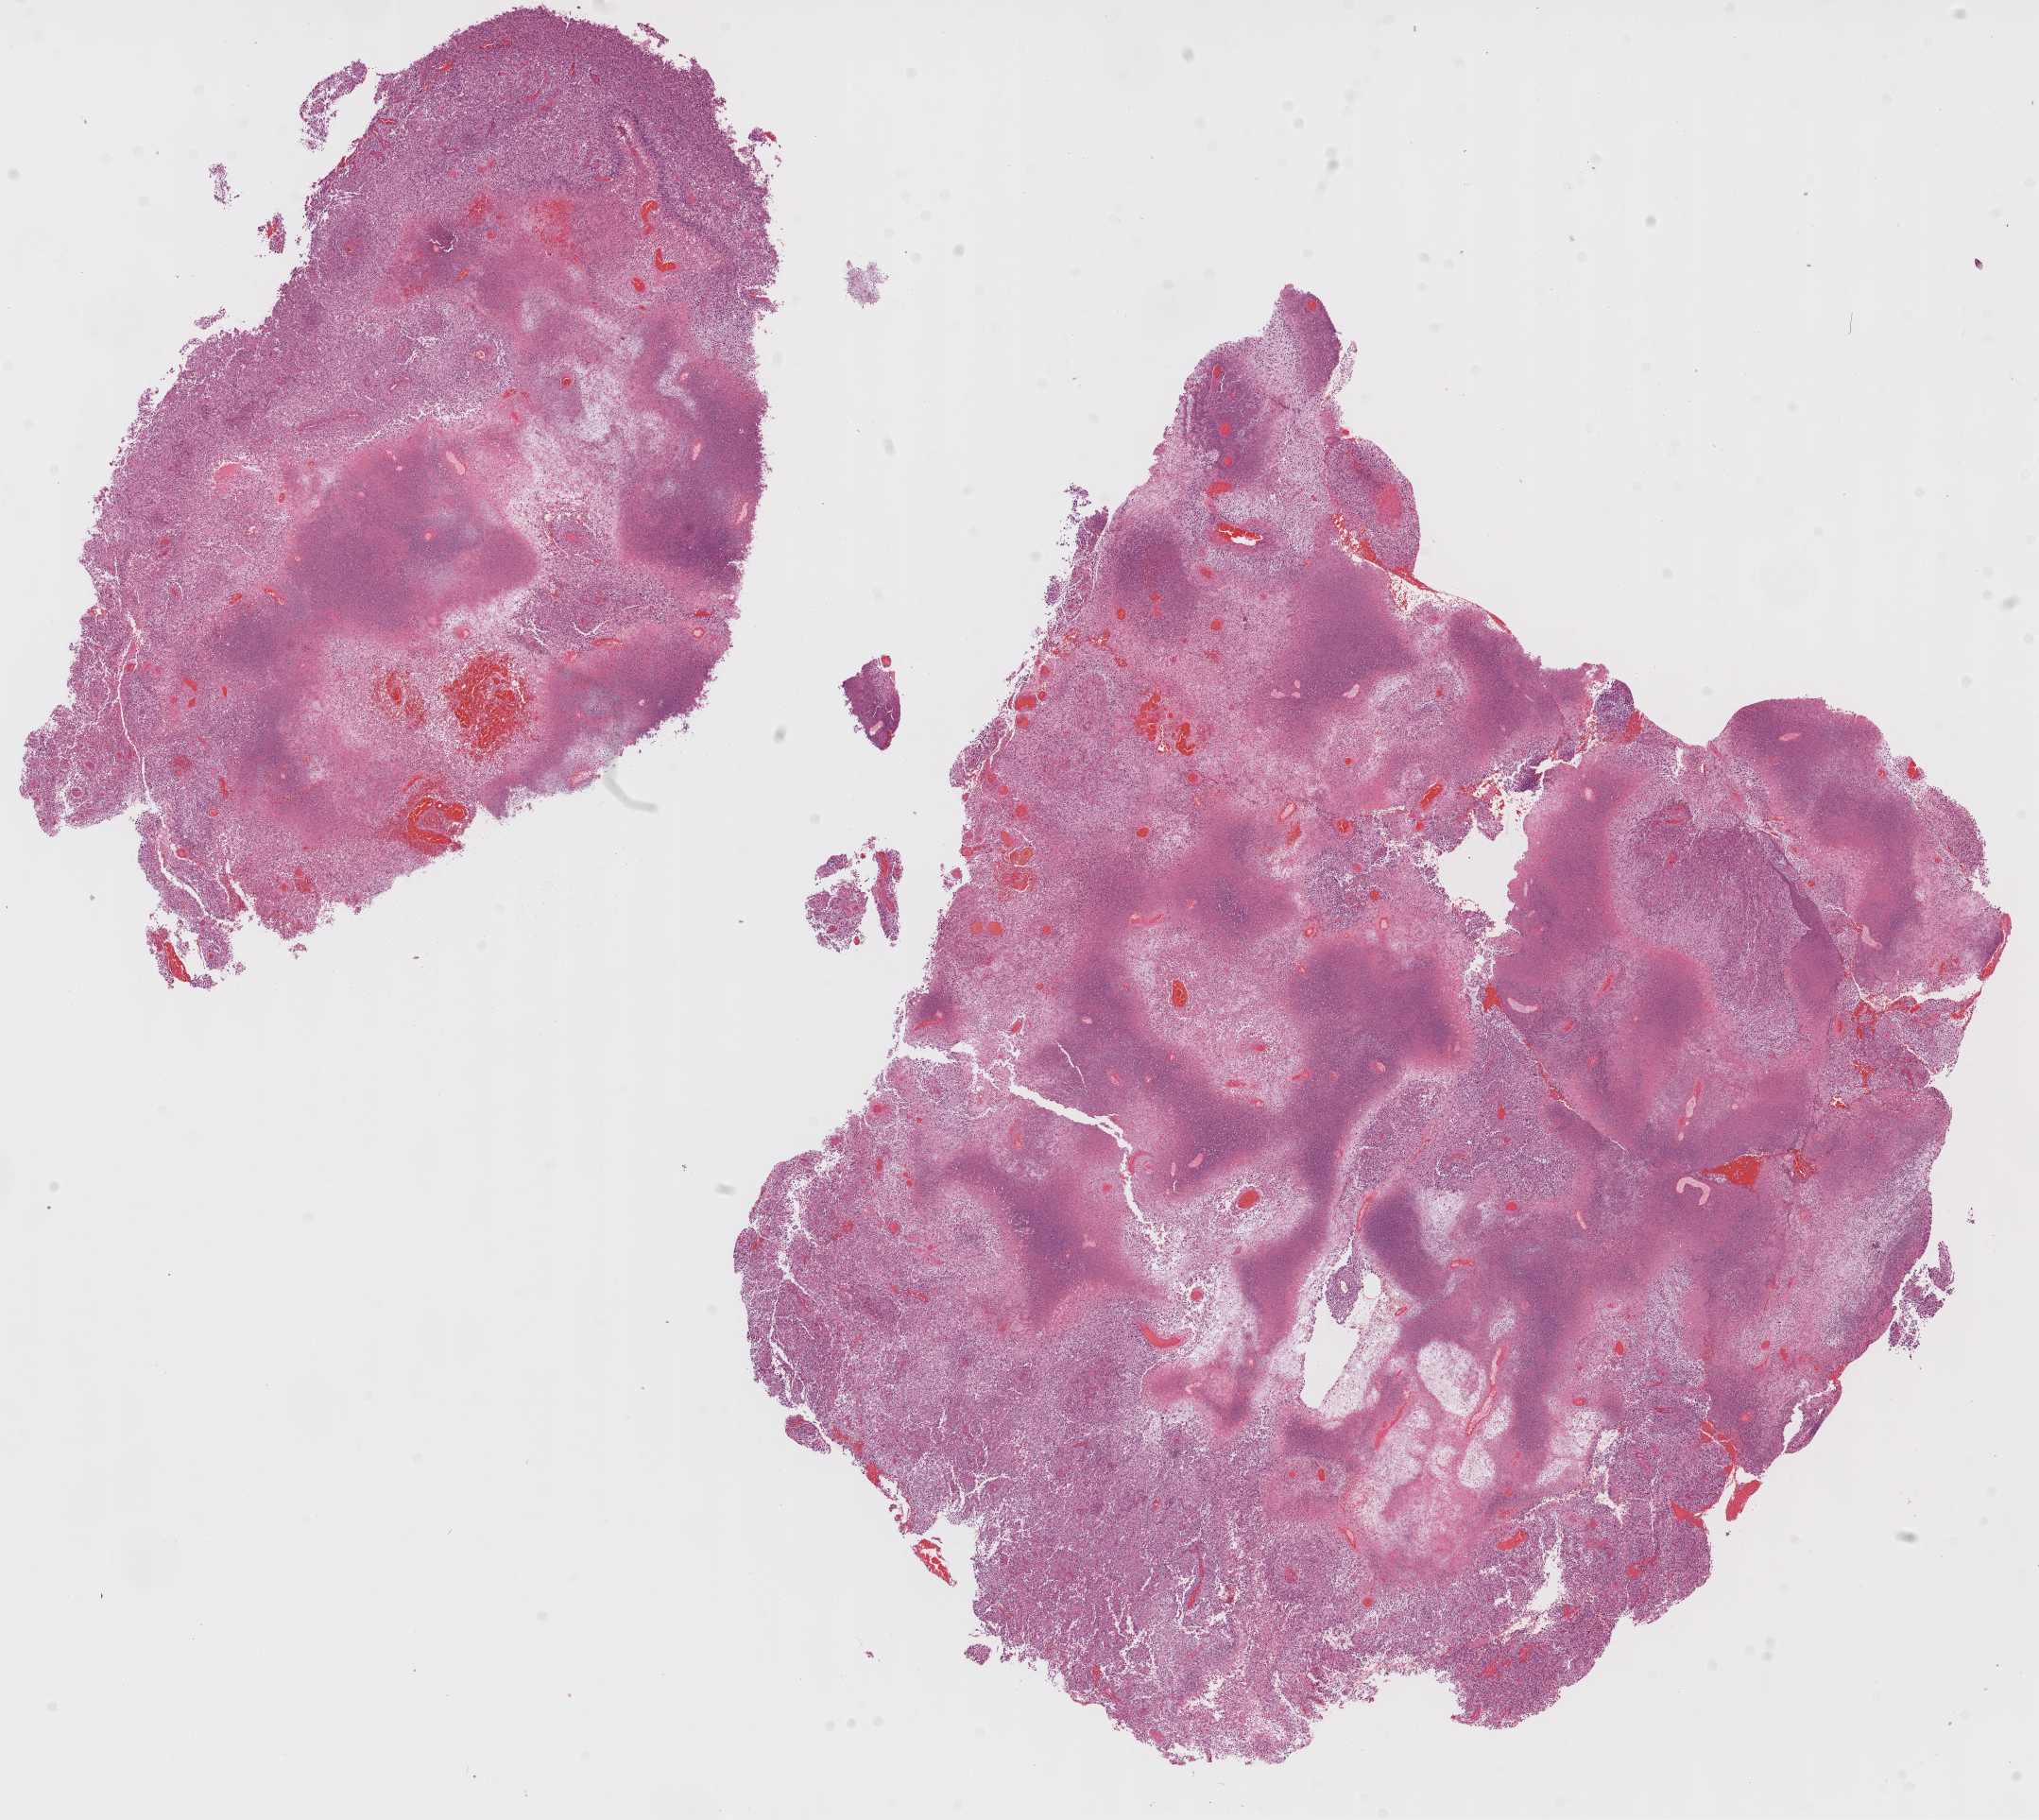
Whole-slide histology image, H&E — a low-resolution overview of the entire scanned area, about 17.4 x 15.5 mm, formalin-fixed paraffin-embedded (FFPE) diagnostic section, sample: primary tumour, brain. Male patient; age at initial diagnosis 51 years.
* histologic diagnosis: Glioblastoma